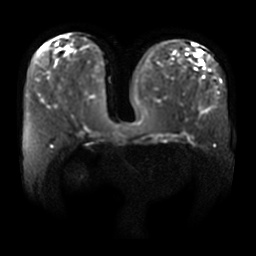
Breast MRI, one axial slice. Slice 15 of 36 in the series (ordered by position). Diffusion-weighted series; image 2 of 4 stored at this slice position (different b-values; order by instance number). 3 T. 256 × 256 image matrix, field of view 400 × 400 mm. Female patient.
Structures marked on this image (outlined manually by an expert reader):
- tumour on diffusion-weighted imaging: box from (x=200, y=61) to (x=204, y=65) px